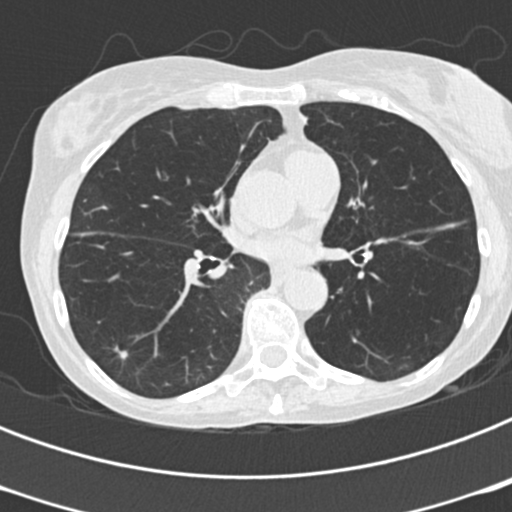
Low-dose screening chest CT, one axial slice; slice 107 of 199 in the series (ordered by position); reconstruction kernel B30f; 120 kVp; lung window (W 1500 / L -600 HU); 2 mm slice thickness; 512 × 512 image matrix.
Outlined on this slice (outlined manually by an expert reader):
- lesion 1 (tumor, lower lobe of right lung): bounding box <113,347,128,359> (left, top, right, bottom; pixels)